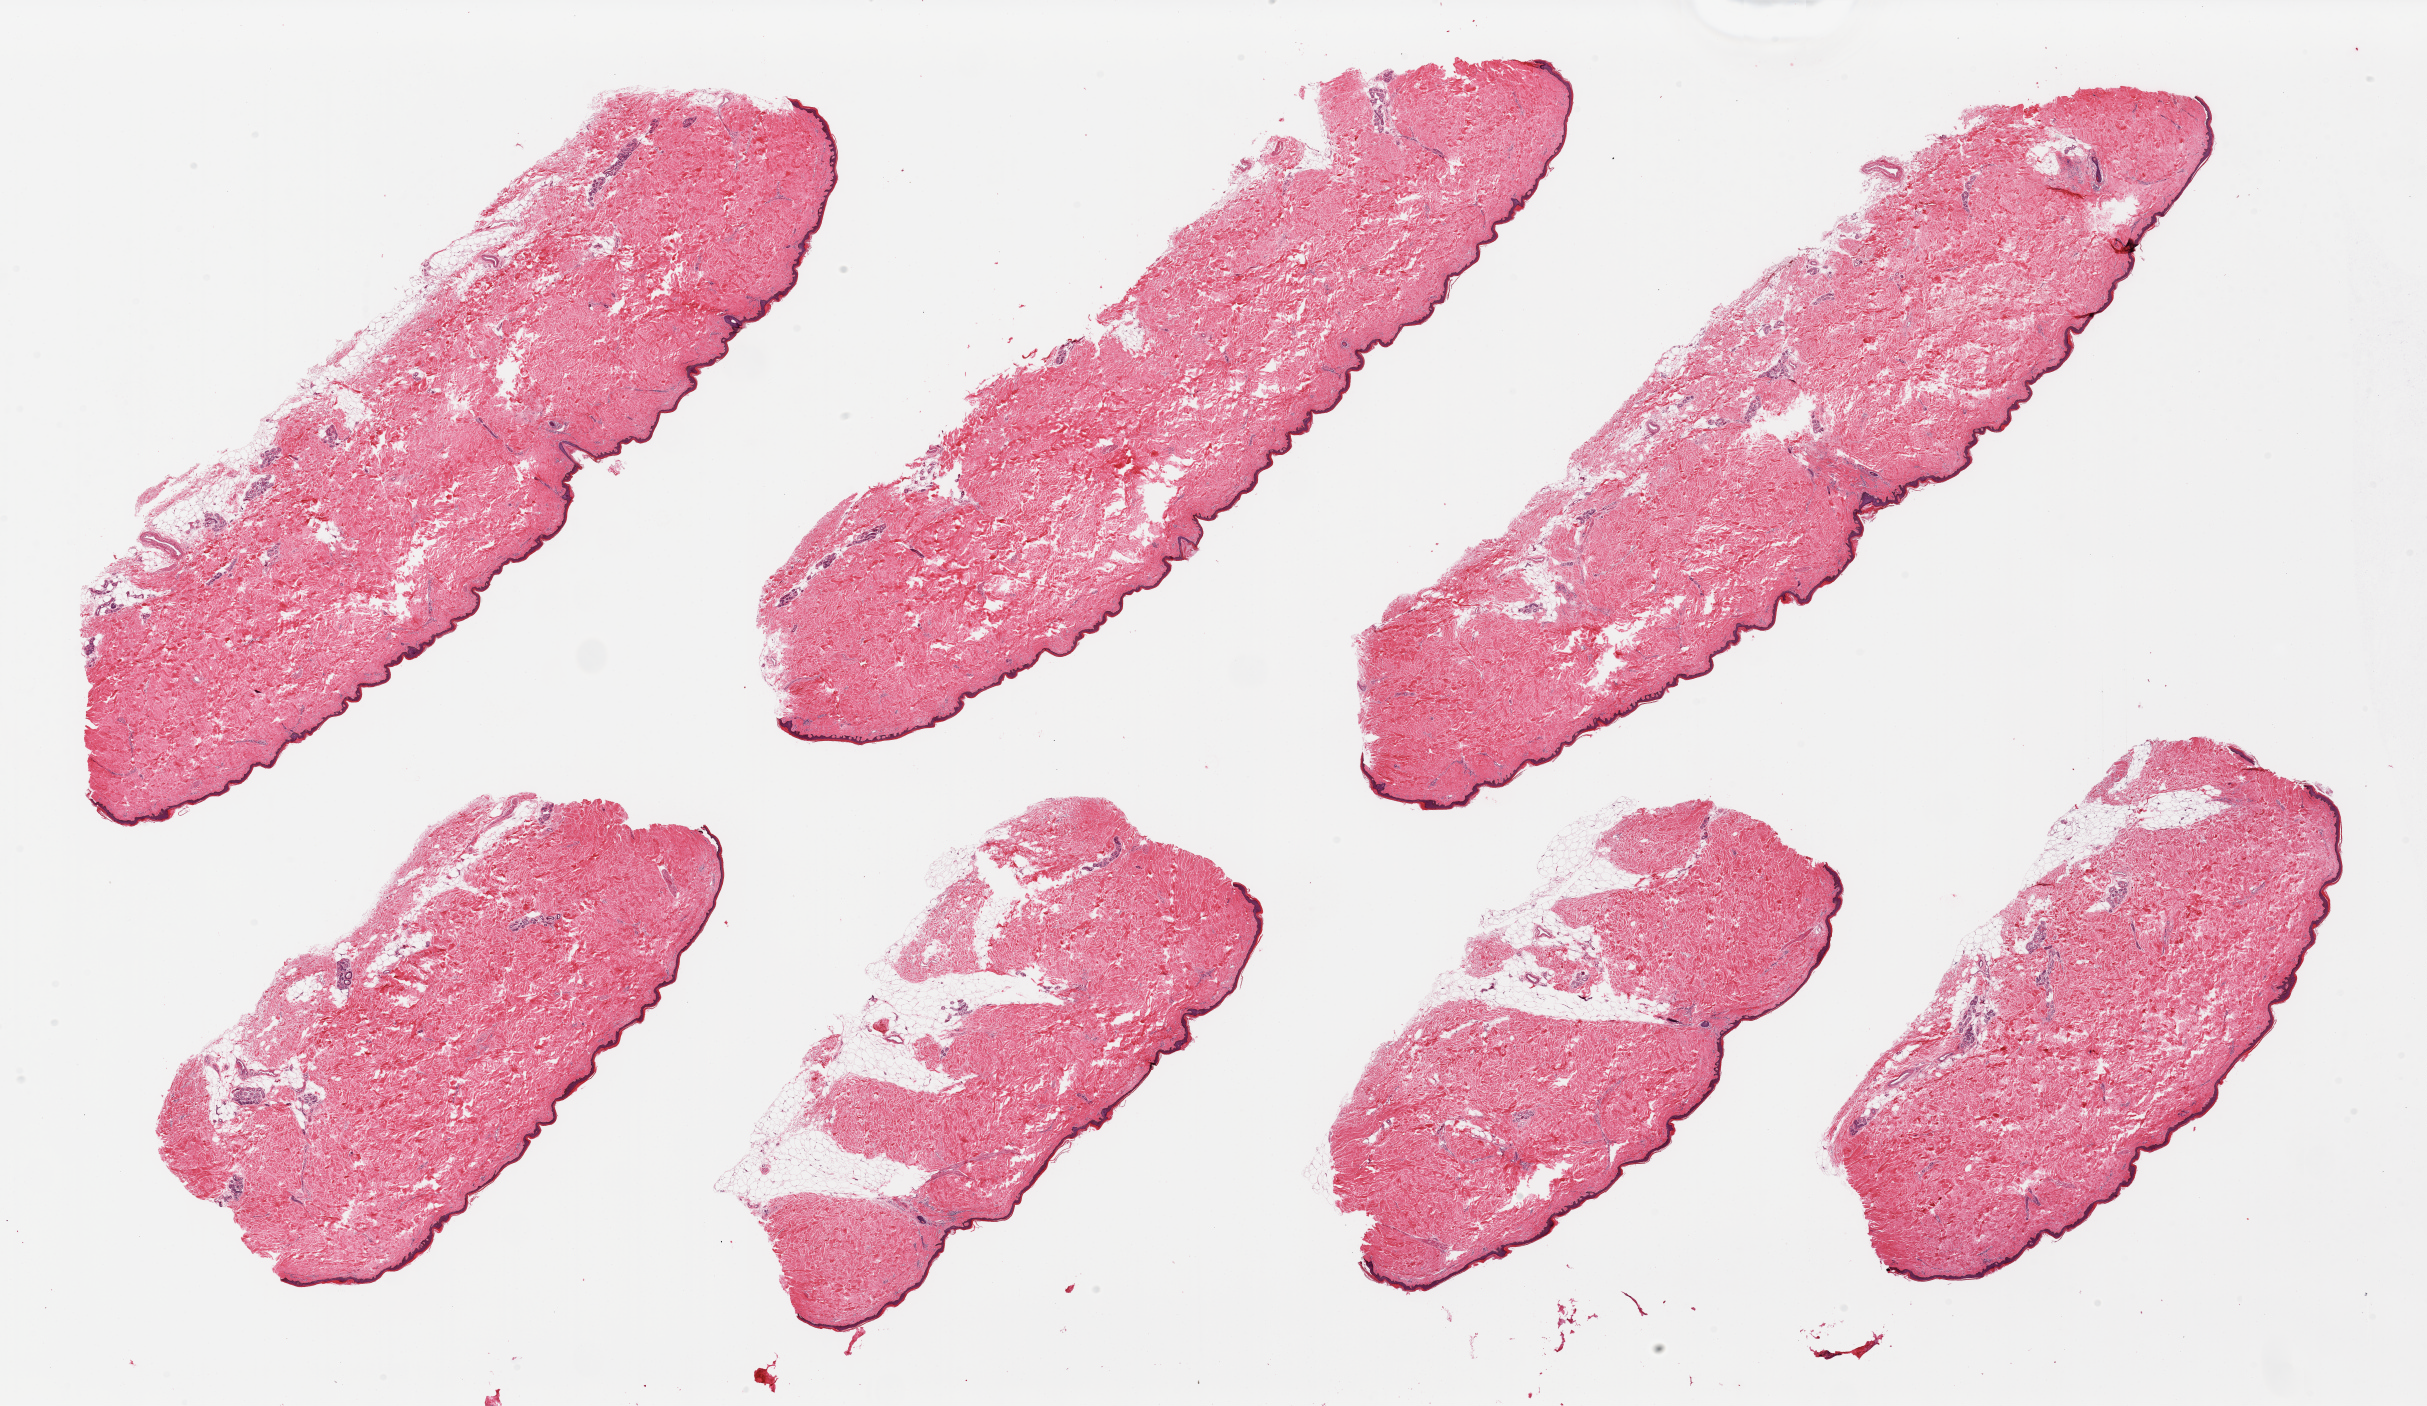
H&E whole-slide image, brightfield — shown as a low-resolution overview of the whole scanned area (about 38.4 x 22.2 mm). PAXgene-fixed, paraffin-embedded tissue. Target tissue: skin of lower leg. Donor tissue sample. Male donor.
Pathologist's review note for this sample: 7 pieces; predominantly well trimmed with minimal attached fat, up to 30% internal fat, epidermis measures 37 microns.